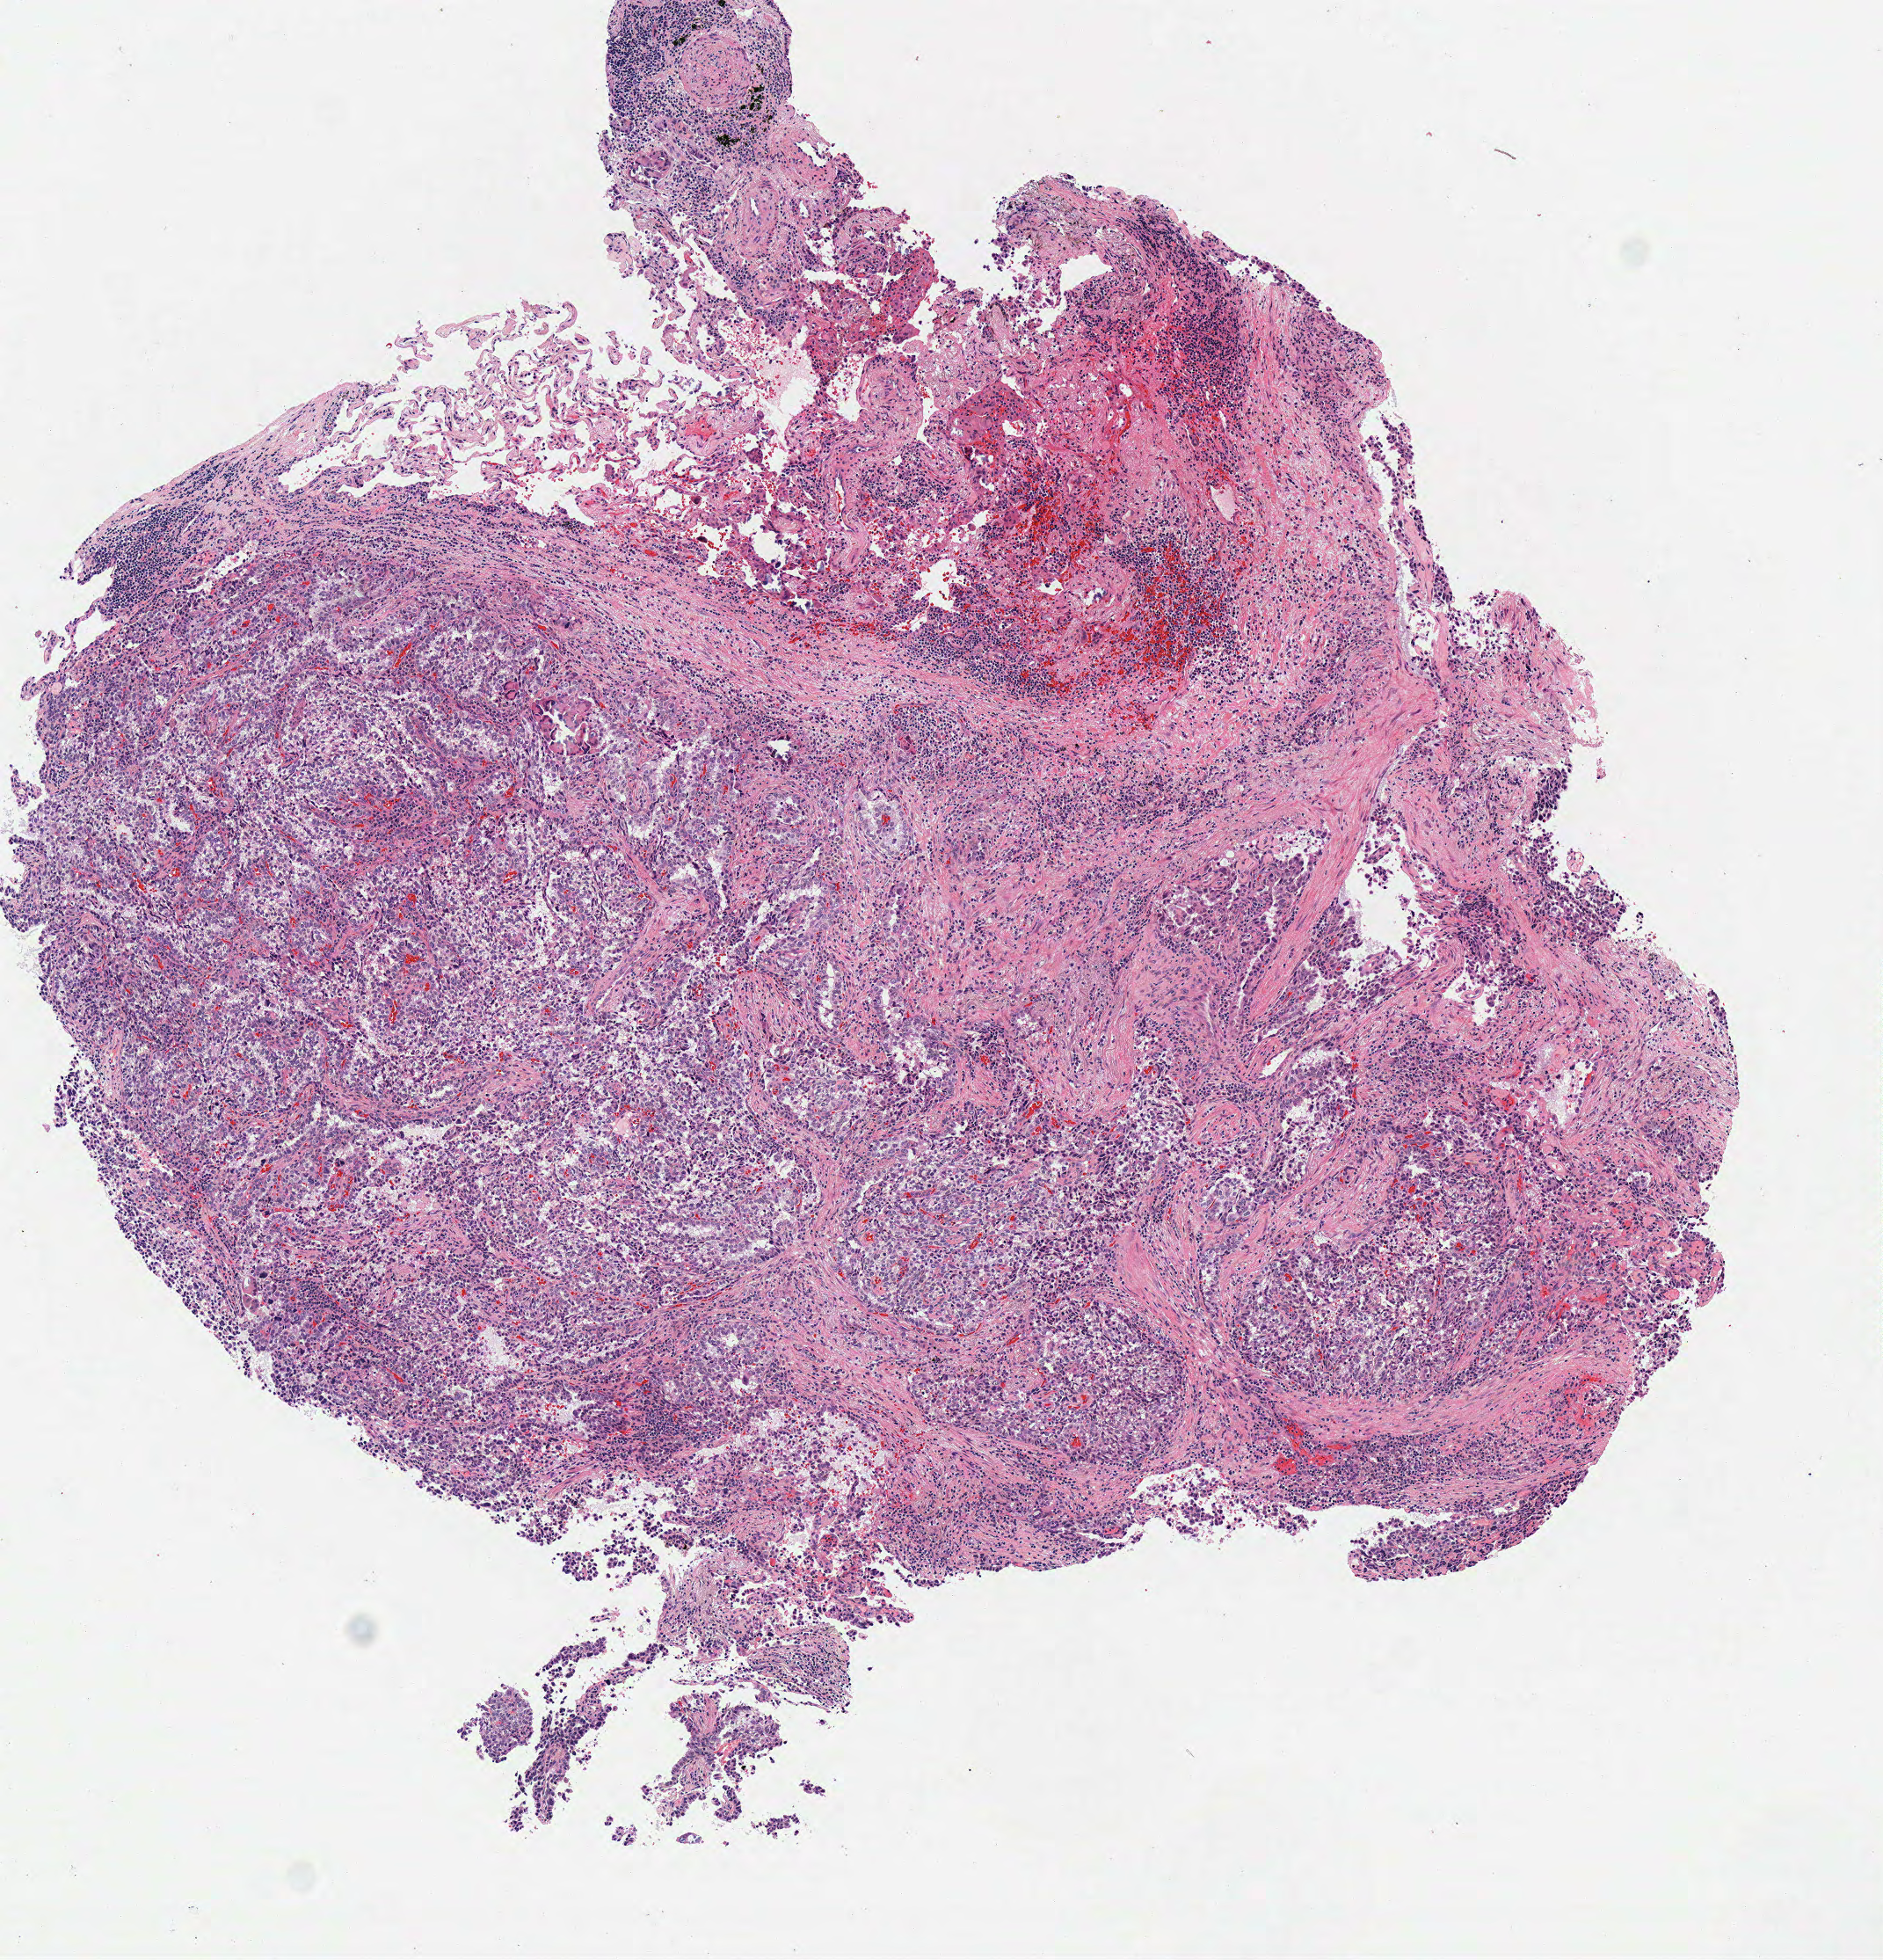
Whole-slide histology image, H&E — low-resolution overview of the scanned area, about 4.2 x 4.4 mm. Frozen section. Sample: primary tumour, lung. Female, age 59 years at initial diagnosis. Pathologist review of this section (percent, as recorded): tumour cells 70%, tumour nuclei 70%, normal cells 15%, stromal cells 15%, necrosis 0%.
- AJCC pathologic stage: IA (7th edition)
- diagnosis: Adenocarcinoma, NOS (upper lobe, lung)